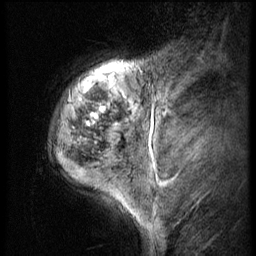
Breast MRI (dynamic contrast-enhanced), one sagittal slice. Slice 10 of 56 in the series (ordered by position). 3 images stored at this slice position (order not interpretable as contrast timing). 1.5 T. TE 4.2 ms, TR 9 ms. 2.5 mm slice thickness. 256 × 256 image matrix. Female patient, age 50 years. From the clinical record (not read from this slice): setting: breast cancer imaged before/during neoadjuvant chemotherapy; receptor status: triple-negative.
Annotated regions visible in this slice (semi-automatically segmented with operator editing):
- analysis volume of interest (the breast-tissue region the enhancement analysis was run in; not a lesion): bounding box <45,50,135,191> (left, top, right, bottom; pixels)
- tumour enhancement mask (voxels above the 140 % enhancement threshold inside the analysis volume of interest): <86,95,117,126>